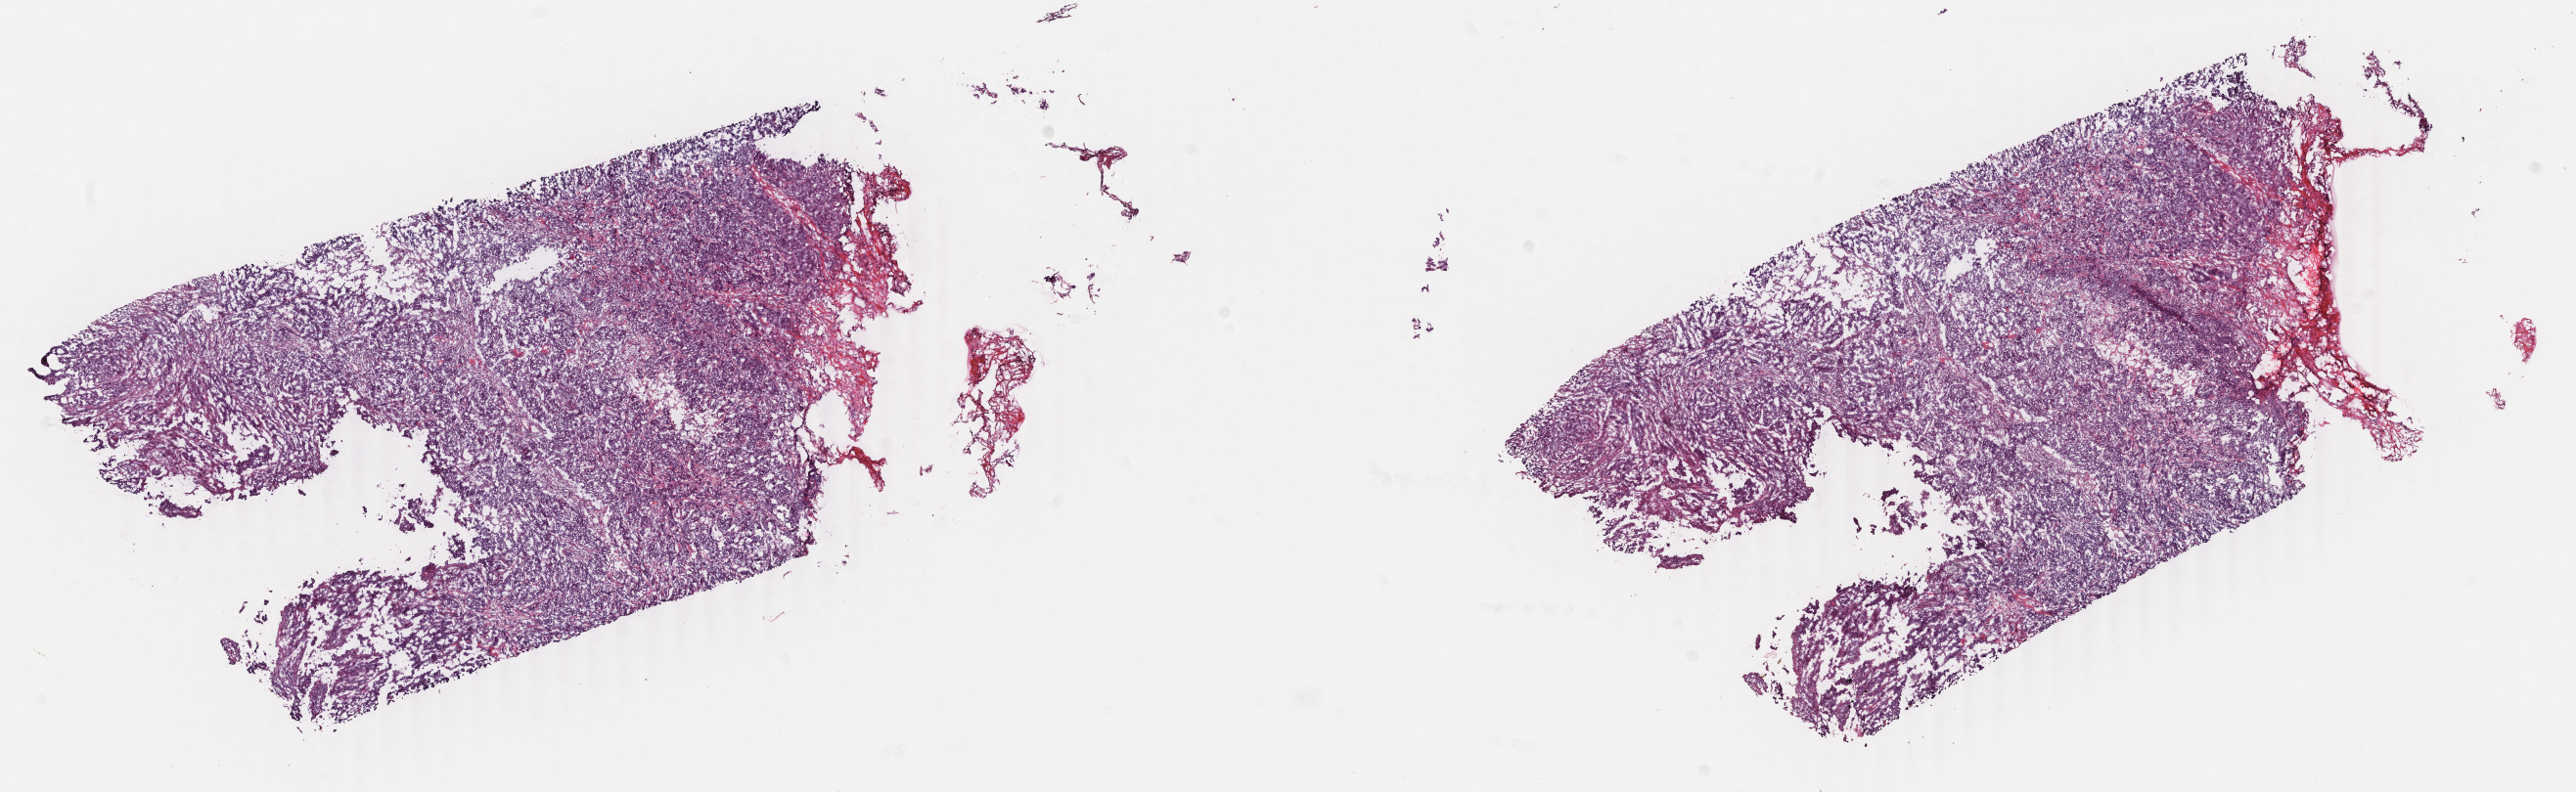
Whole-slide histology image, Hematoxylin and eosin (H&E) stained, whole scanned area (about 20.9 x 6.4 mm, from a 40x scan) shown as a low-resolution overview. Frozen section from the top of the tissue portion. Breast, primary tumour sample. Female, age 67 years at initial diagnosis. Composition of this section per pathologist review: tumour cells 95%, tumour nuclei 97%, normal cells 0%, stromal cells 5%, necrosis 0%. Inflammatory infiltration, as recorded: lymphocyte infiltration 0%, monocyte infiltration 0%, neutrophil infiltration 0%.
- pathologic diagnosis: Infiltrating duct carcinoma, NOS
- AJCC pathologic stage: IIA